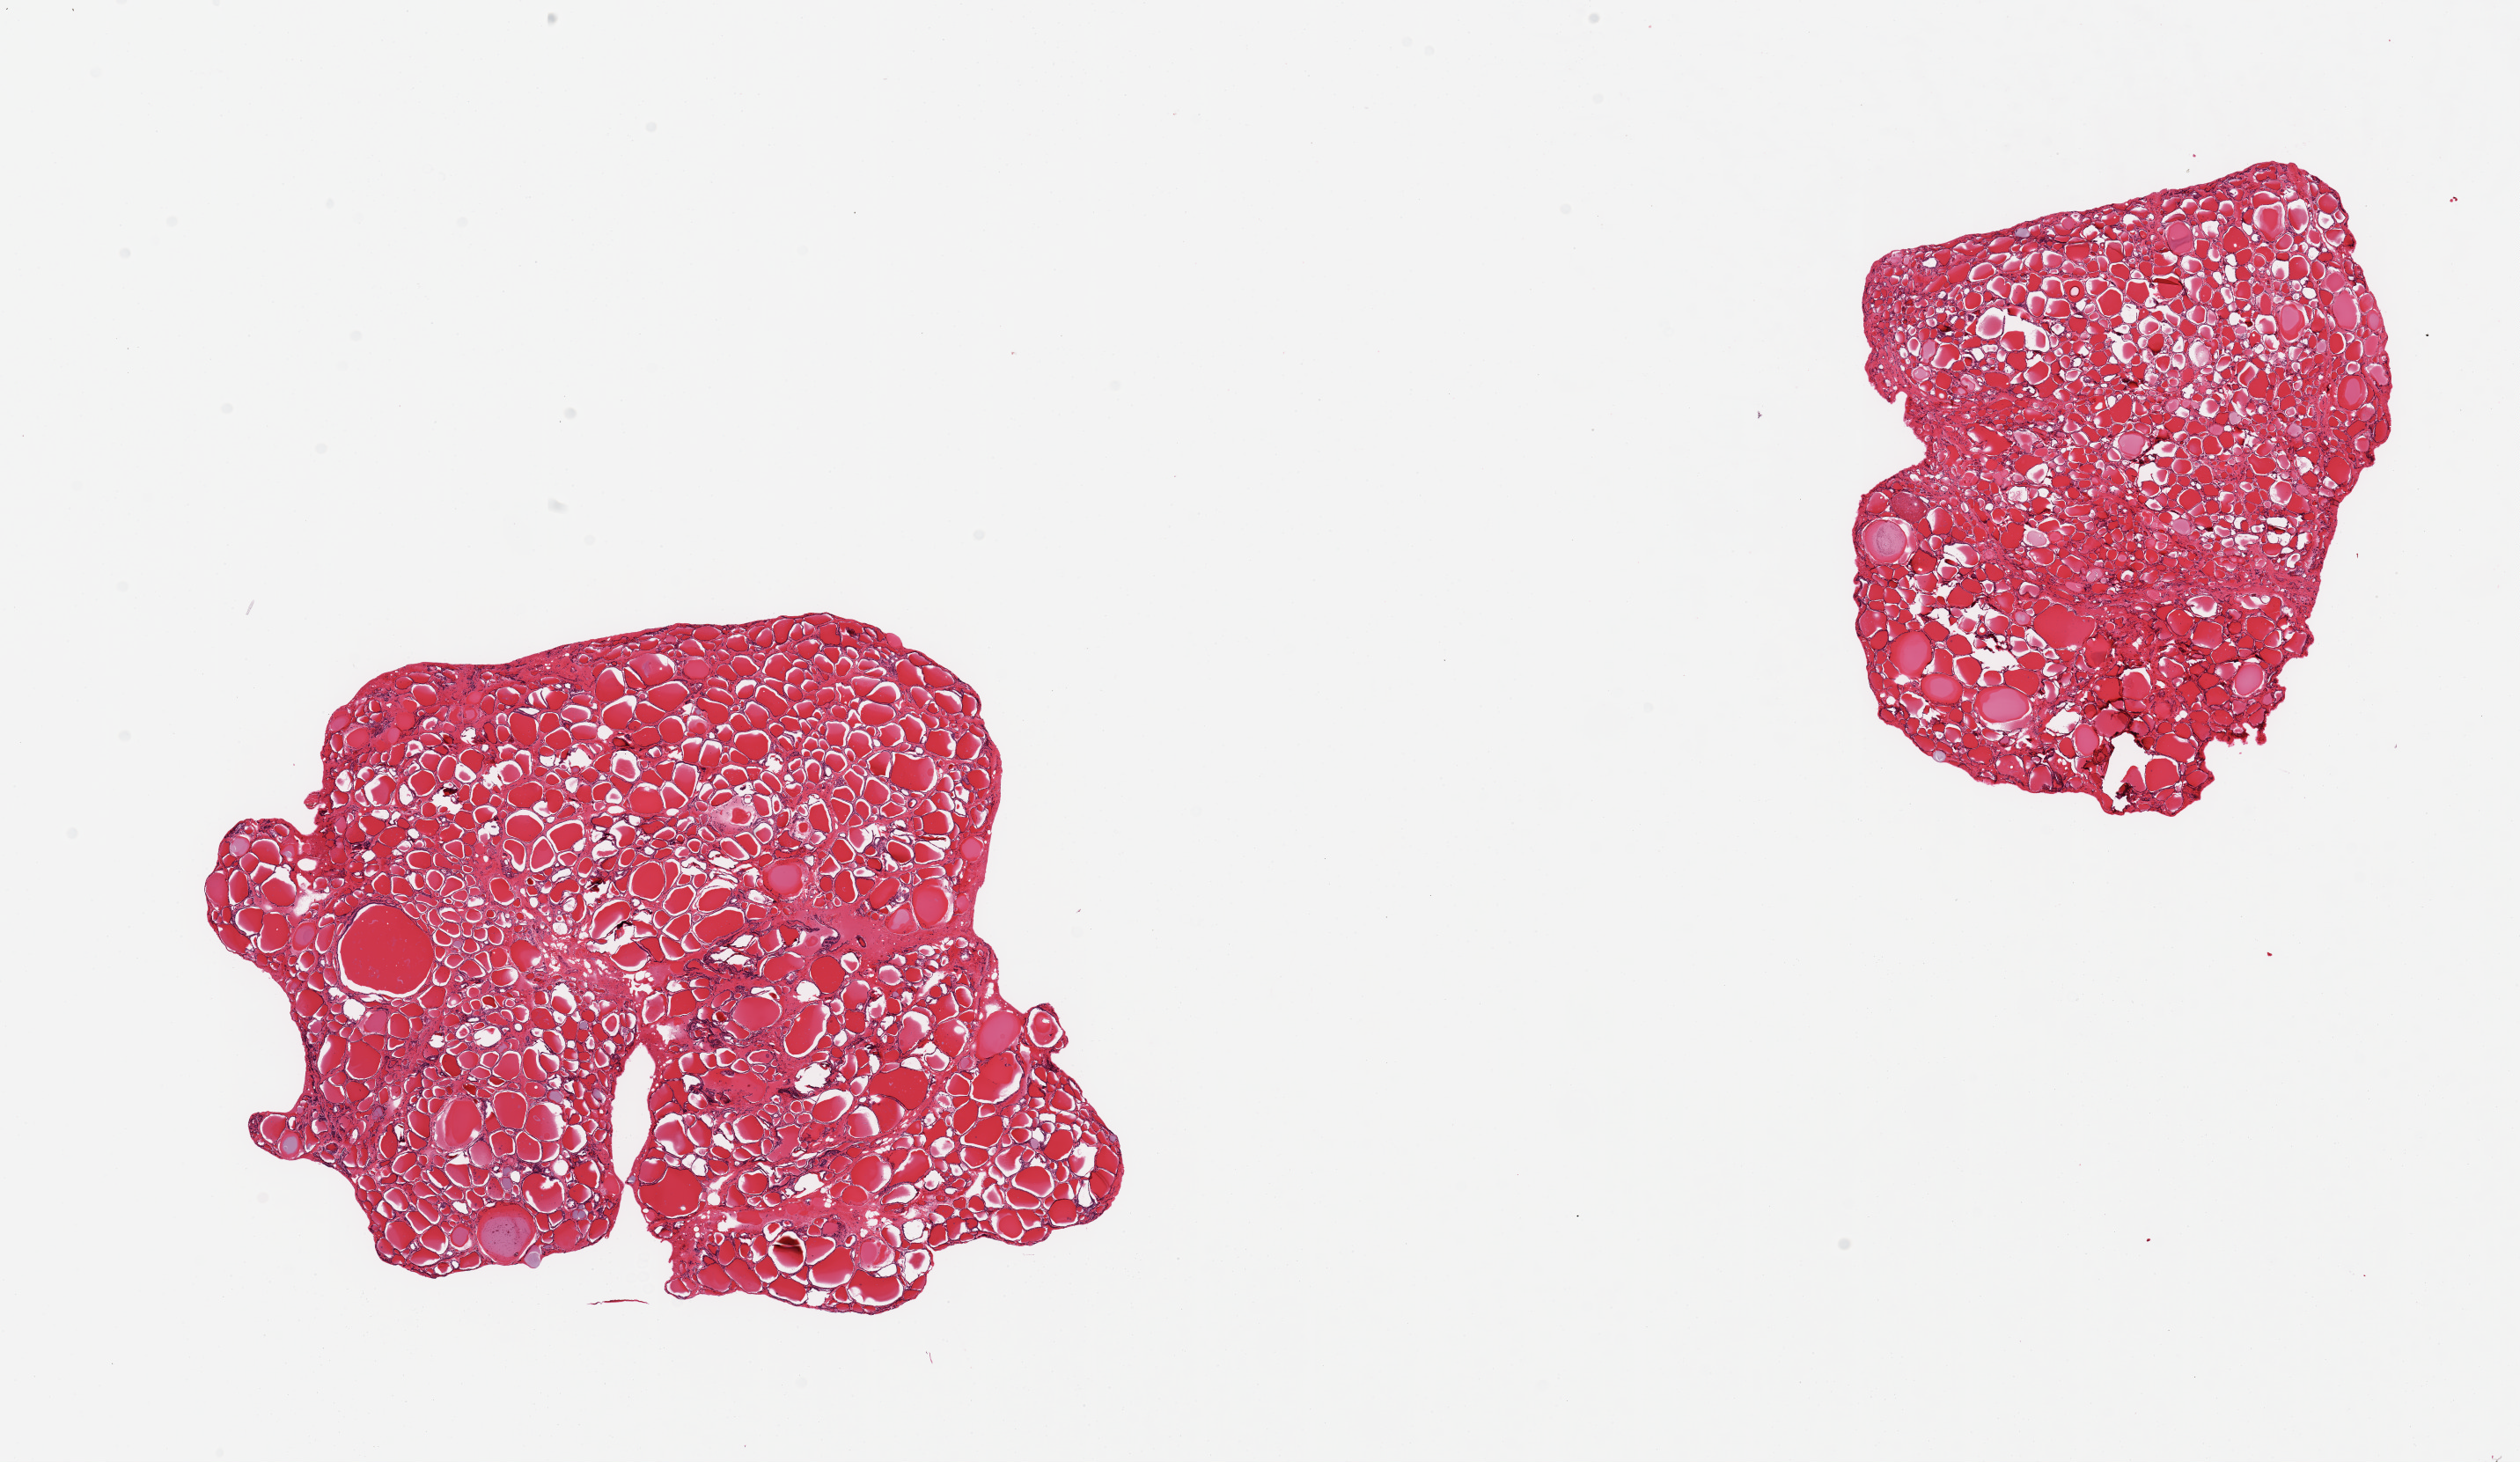
Hematoxylin and eosin (H&E) whole-slide image, brightfield — low-resolution overview of the scanned area, about 22.6 x 13.1 mm (from a 20x scan). PAXgene-fixed paraffin-embedded (PFPE) section. Sampled site (target tissue): thyroid. Donor tissue sample.
Reviewer comment on this tissue sample: 2 pieces, no significant abnormalities; few incidental colloid cysts.